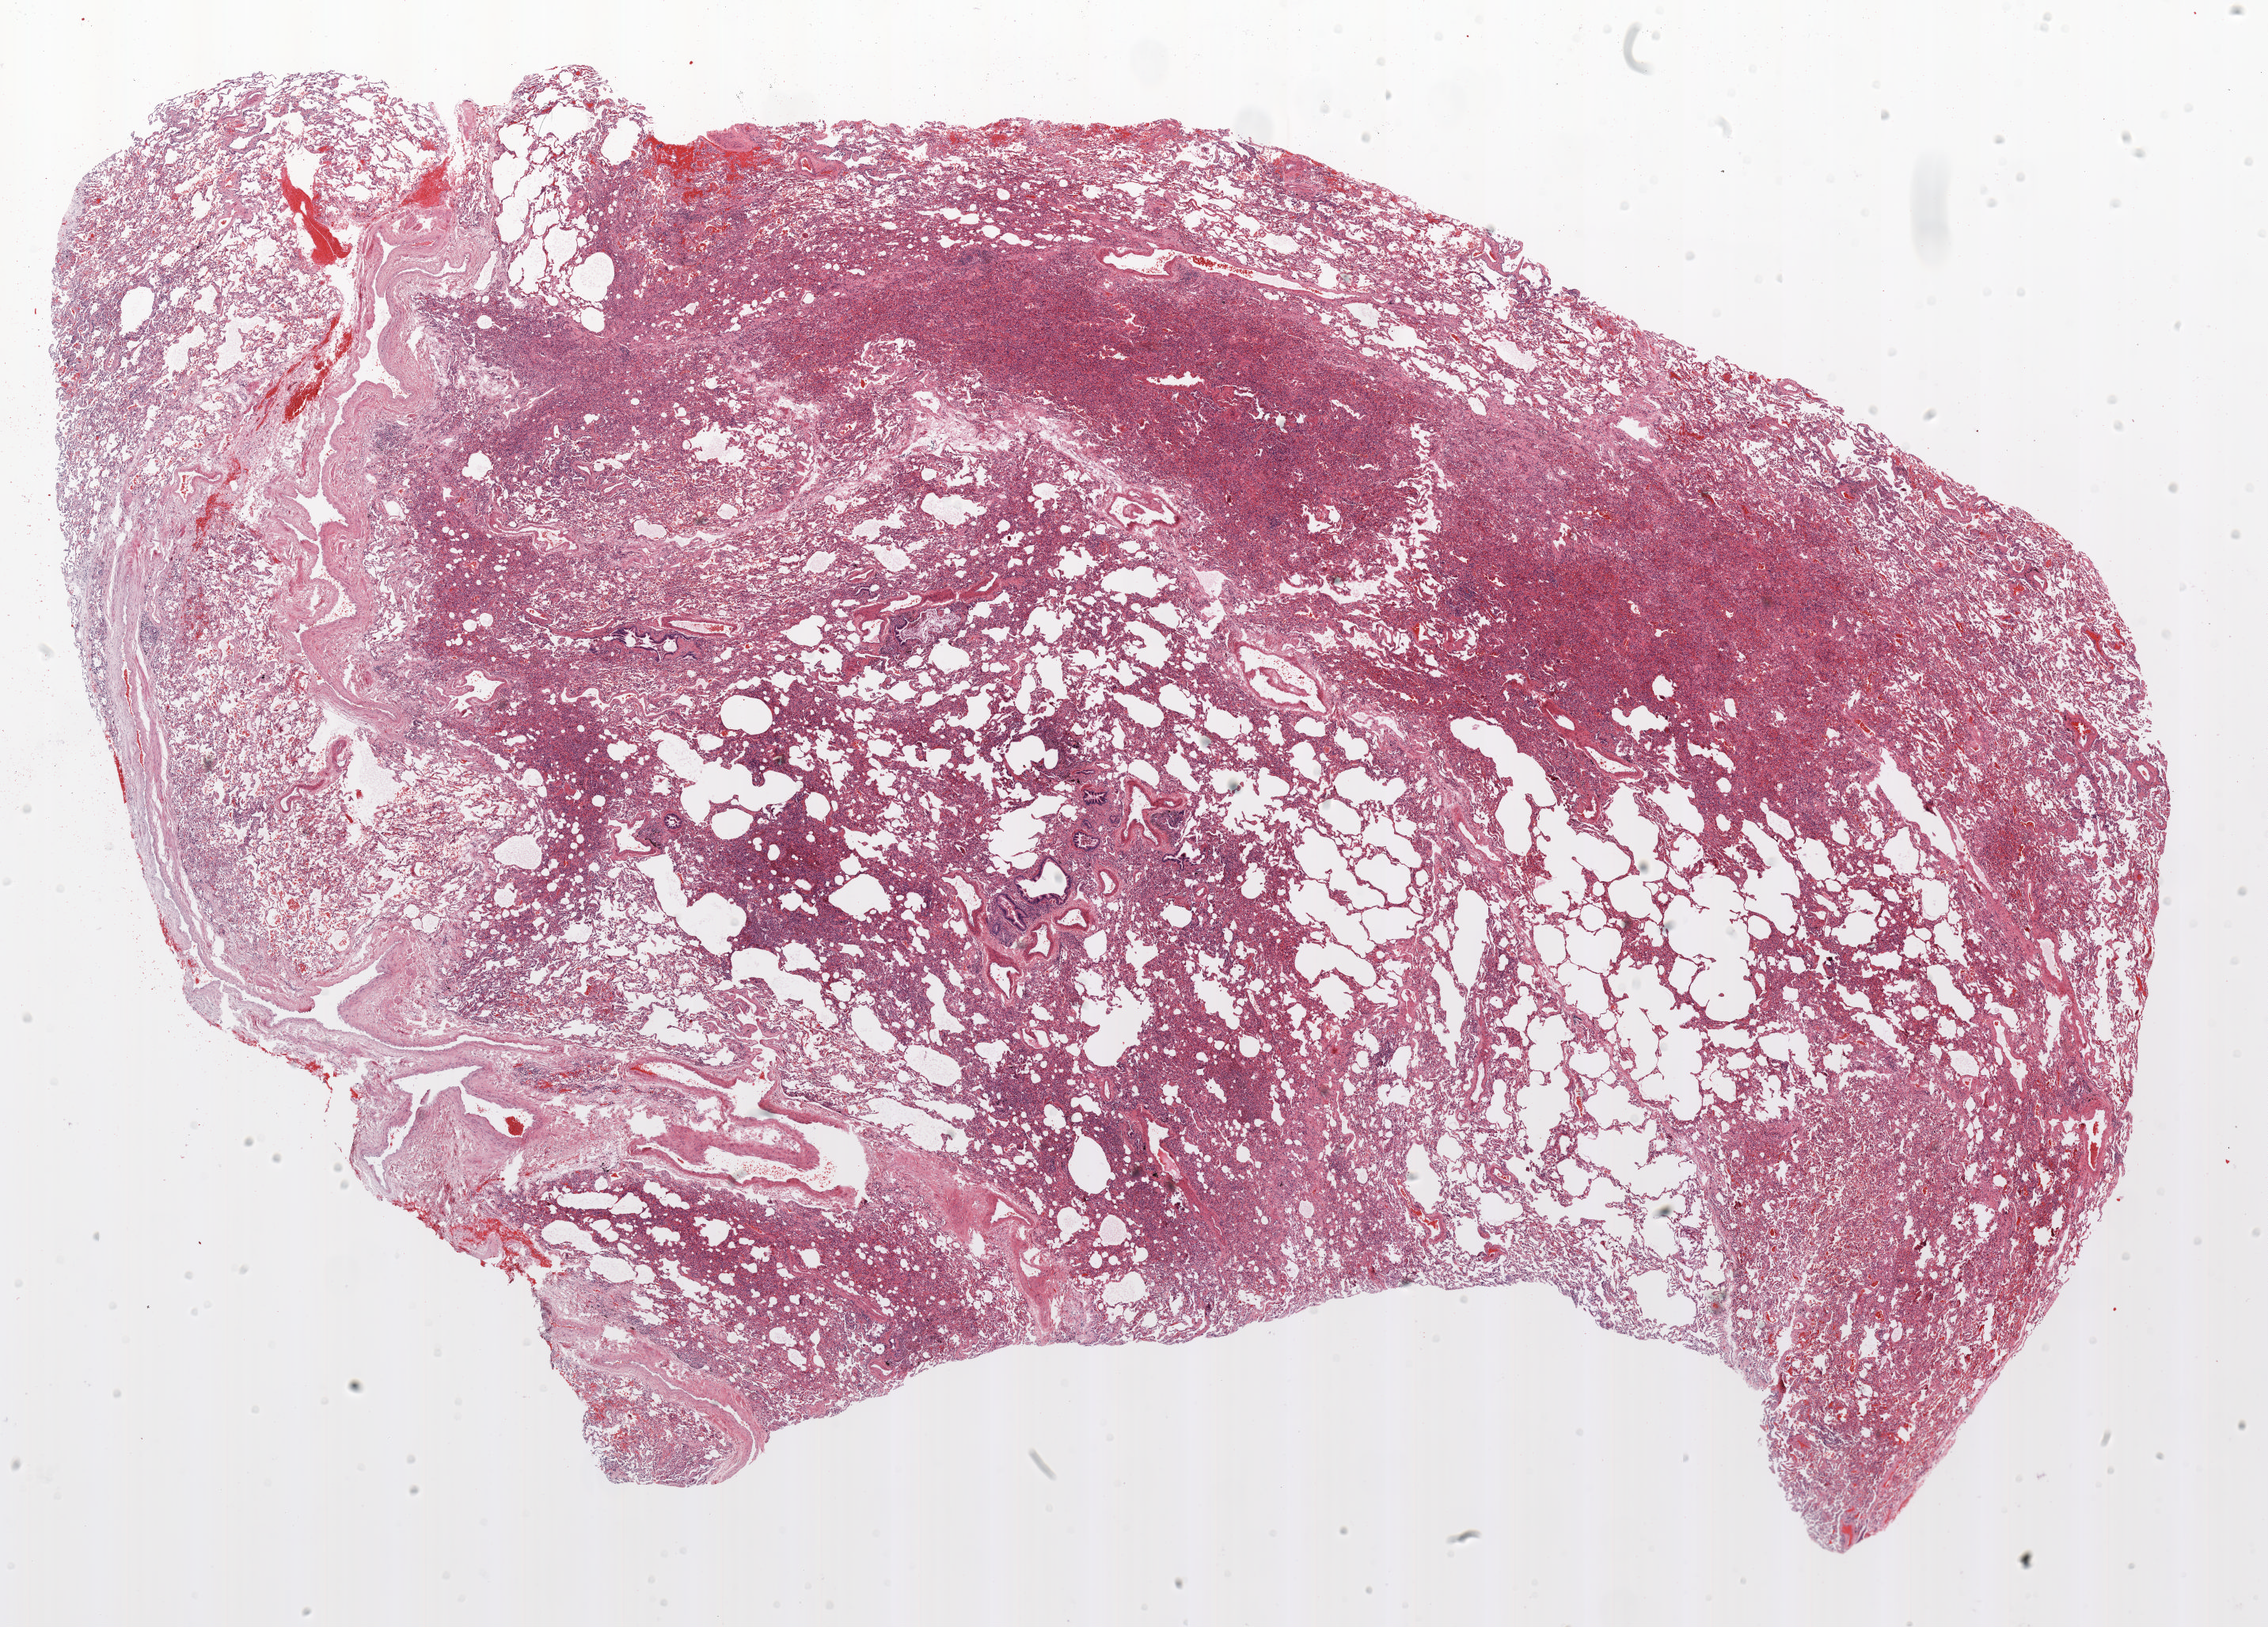
H&E-stained whole-slide image, shown as a low-resolution overview of the whole scanned area (about 23.0 x 16.5 mm). Formalin-fixed paraffin-embedded (FFPE) section. Lung tissue. Female, age 65 at enrolment. Current smoker at enrolment. Grade: poorly differentiated (G3).
- stage (AJCC 6th edition): IA
- participant's lung-cancer diagnosis: Large cell carcinoma, NOS
- primary tumour location (clinical record): right upper lobe
- tumour size (pathology): 20 mm